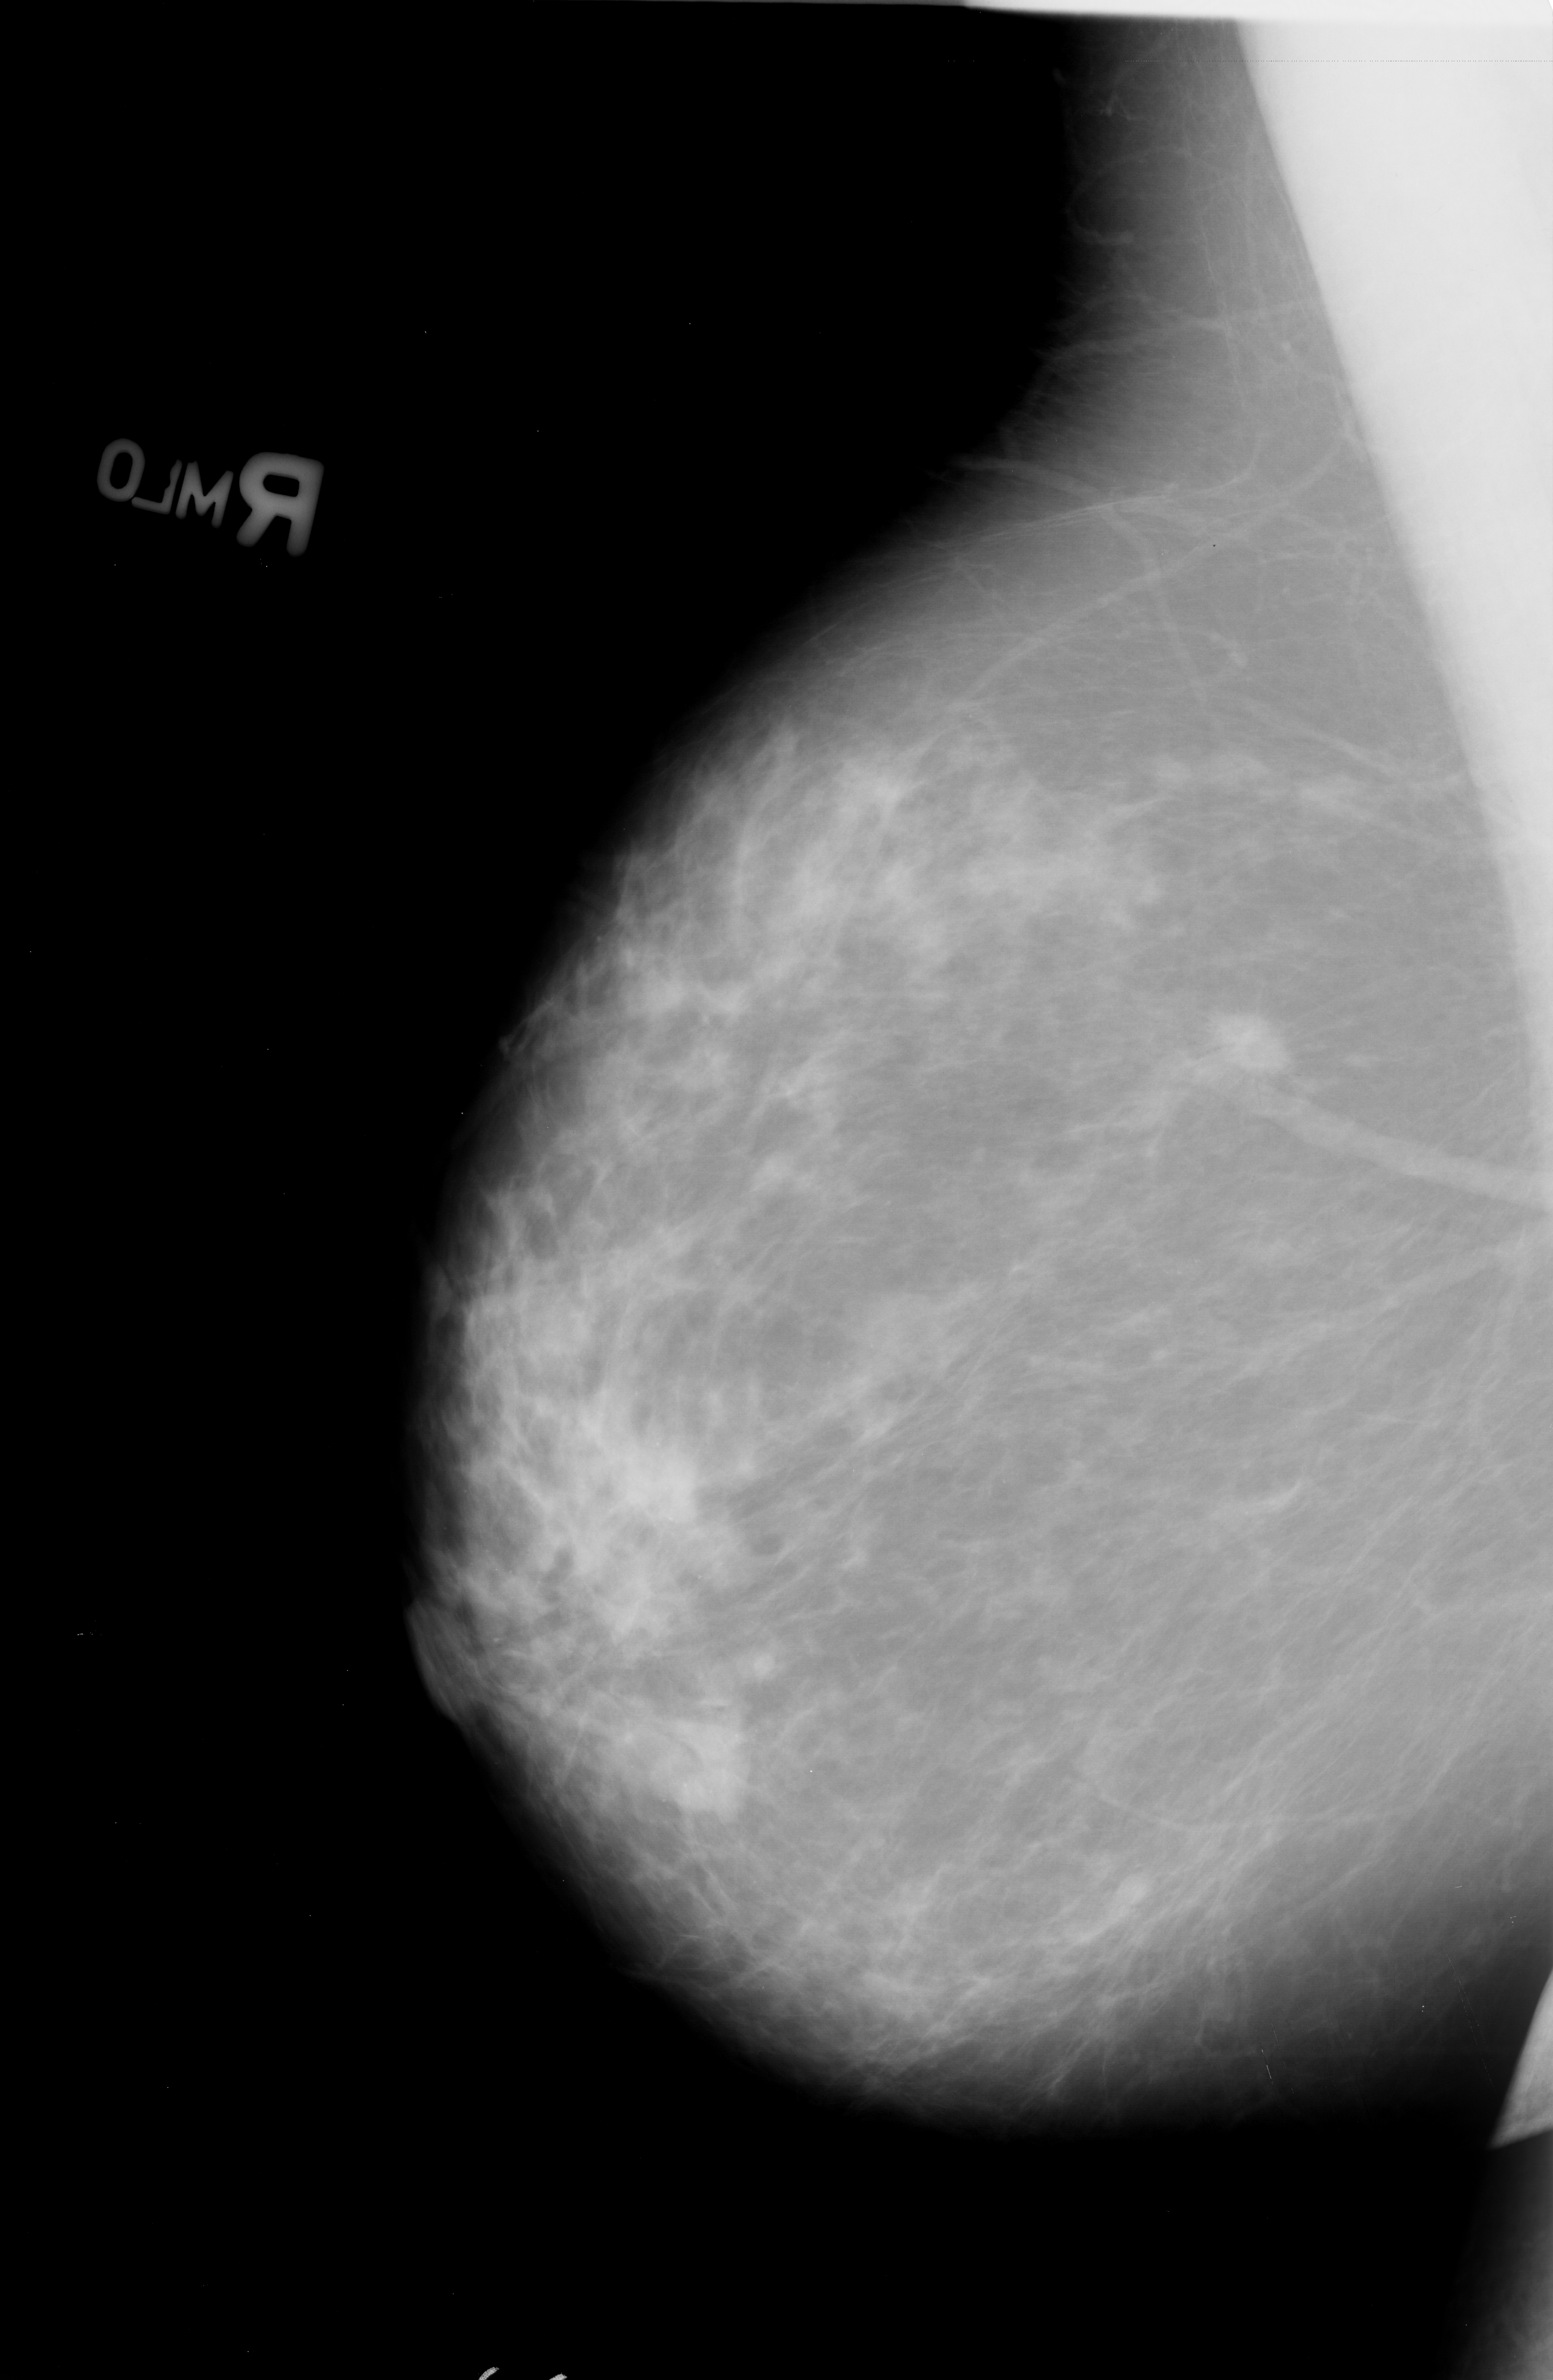
Mammogram (digitized film); right breast; mediolateral oblique (MLO) view; breast composition: scattered fibroglandular densities (BI-RADS density category 2 of 4).
Marked abnormality: mass, shape oval, margins spiculated; BI-RADS assessment category 5; subtlety rating 4 on a 1 (subtle) to 5 (obvious) scale; pathology (as recorded): malignant.